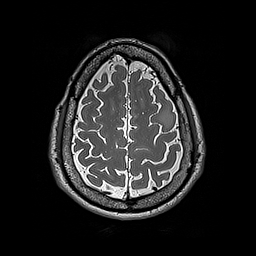
Brain MRI from a brain-tumour surgery series, one axial slice. Position 59 of 192 along the scan axis. 1 mm slice thickness. 256 × 256 image matrix, field of view 250 × 250 mm. From the clinical record (not read from this slice): histopathology: Astrocytoma; WHO grade: 2; IDH mutation: yes.
Outlined on this slice (outlined manually by an expert reader):
- tumour: bounding box <158,107,173,128> (left, top, right, bottom; pixels)